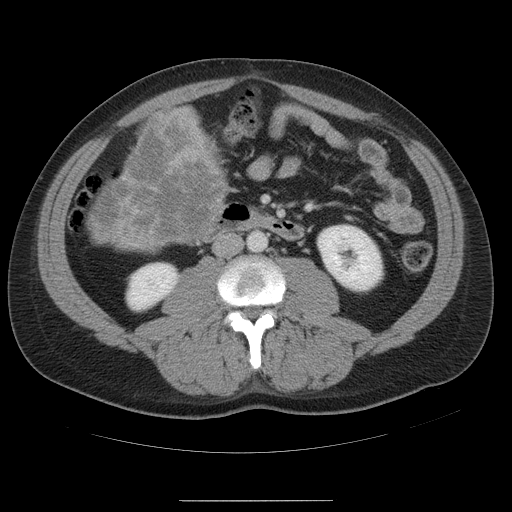
Contrast-enhanced abdominal CT, one axial slice. Position 11 of 54 along the scan axis. 120 kVp. Intravenous contrast given. Soft-tissue window (W 400 / L 40 HU). 5 mm slice thickness. 512 × 512 image matrix. Male patient, age 40 years. Case-level facts recorded for this patient, not image findings: diagnosis: colorectal cancer liver metastases, imaged before liver resection; multiple liver metastases: no; largest metastasis: 15 cm; chemotherapy before resection: no.
Structures marked on this image (expert manual segmentation):
- liver: bounding box <89,107,228,251> (left, top, right, bottom; pixels)
- liver metastasis: <90,114,227,247>